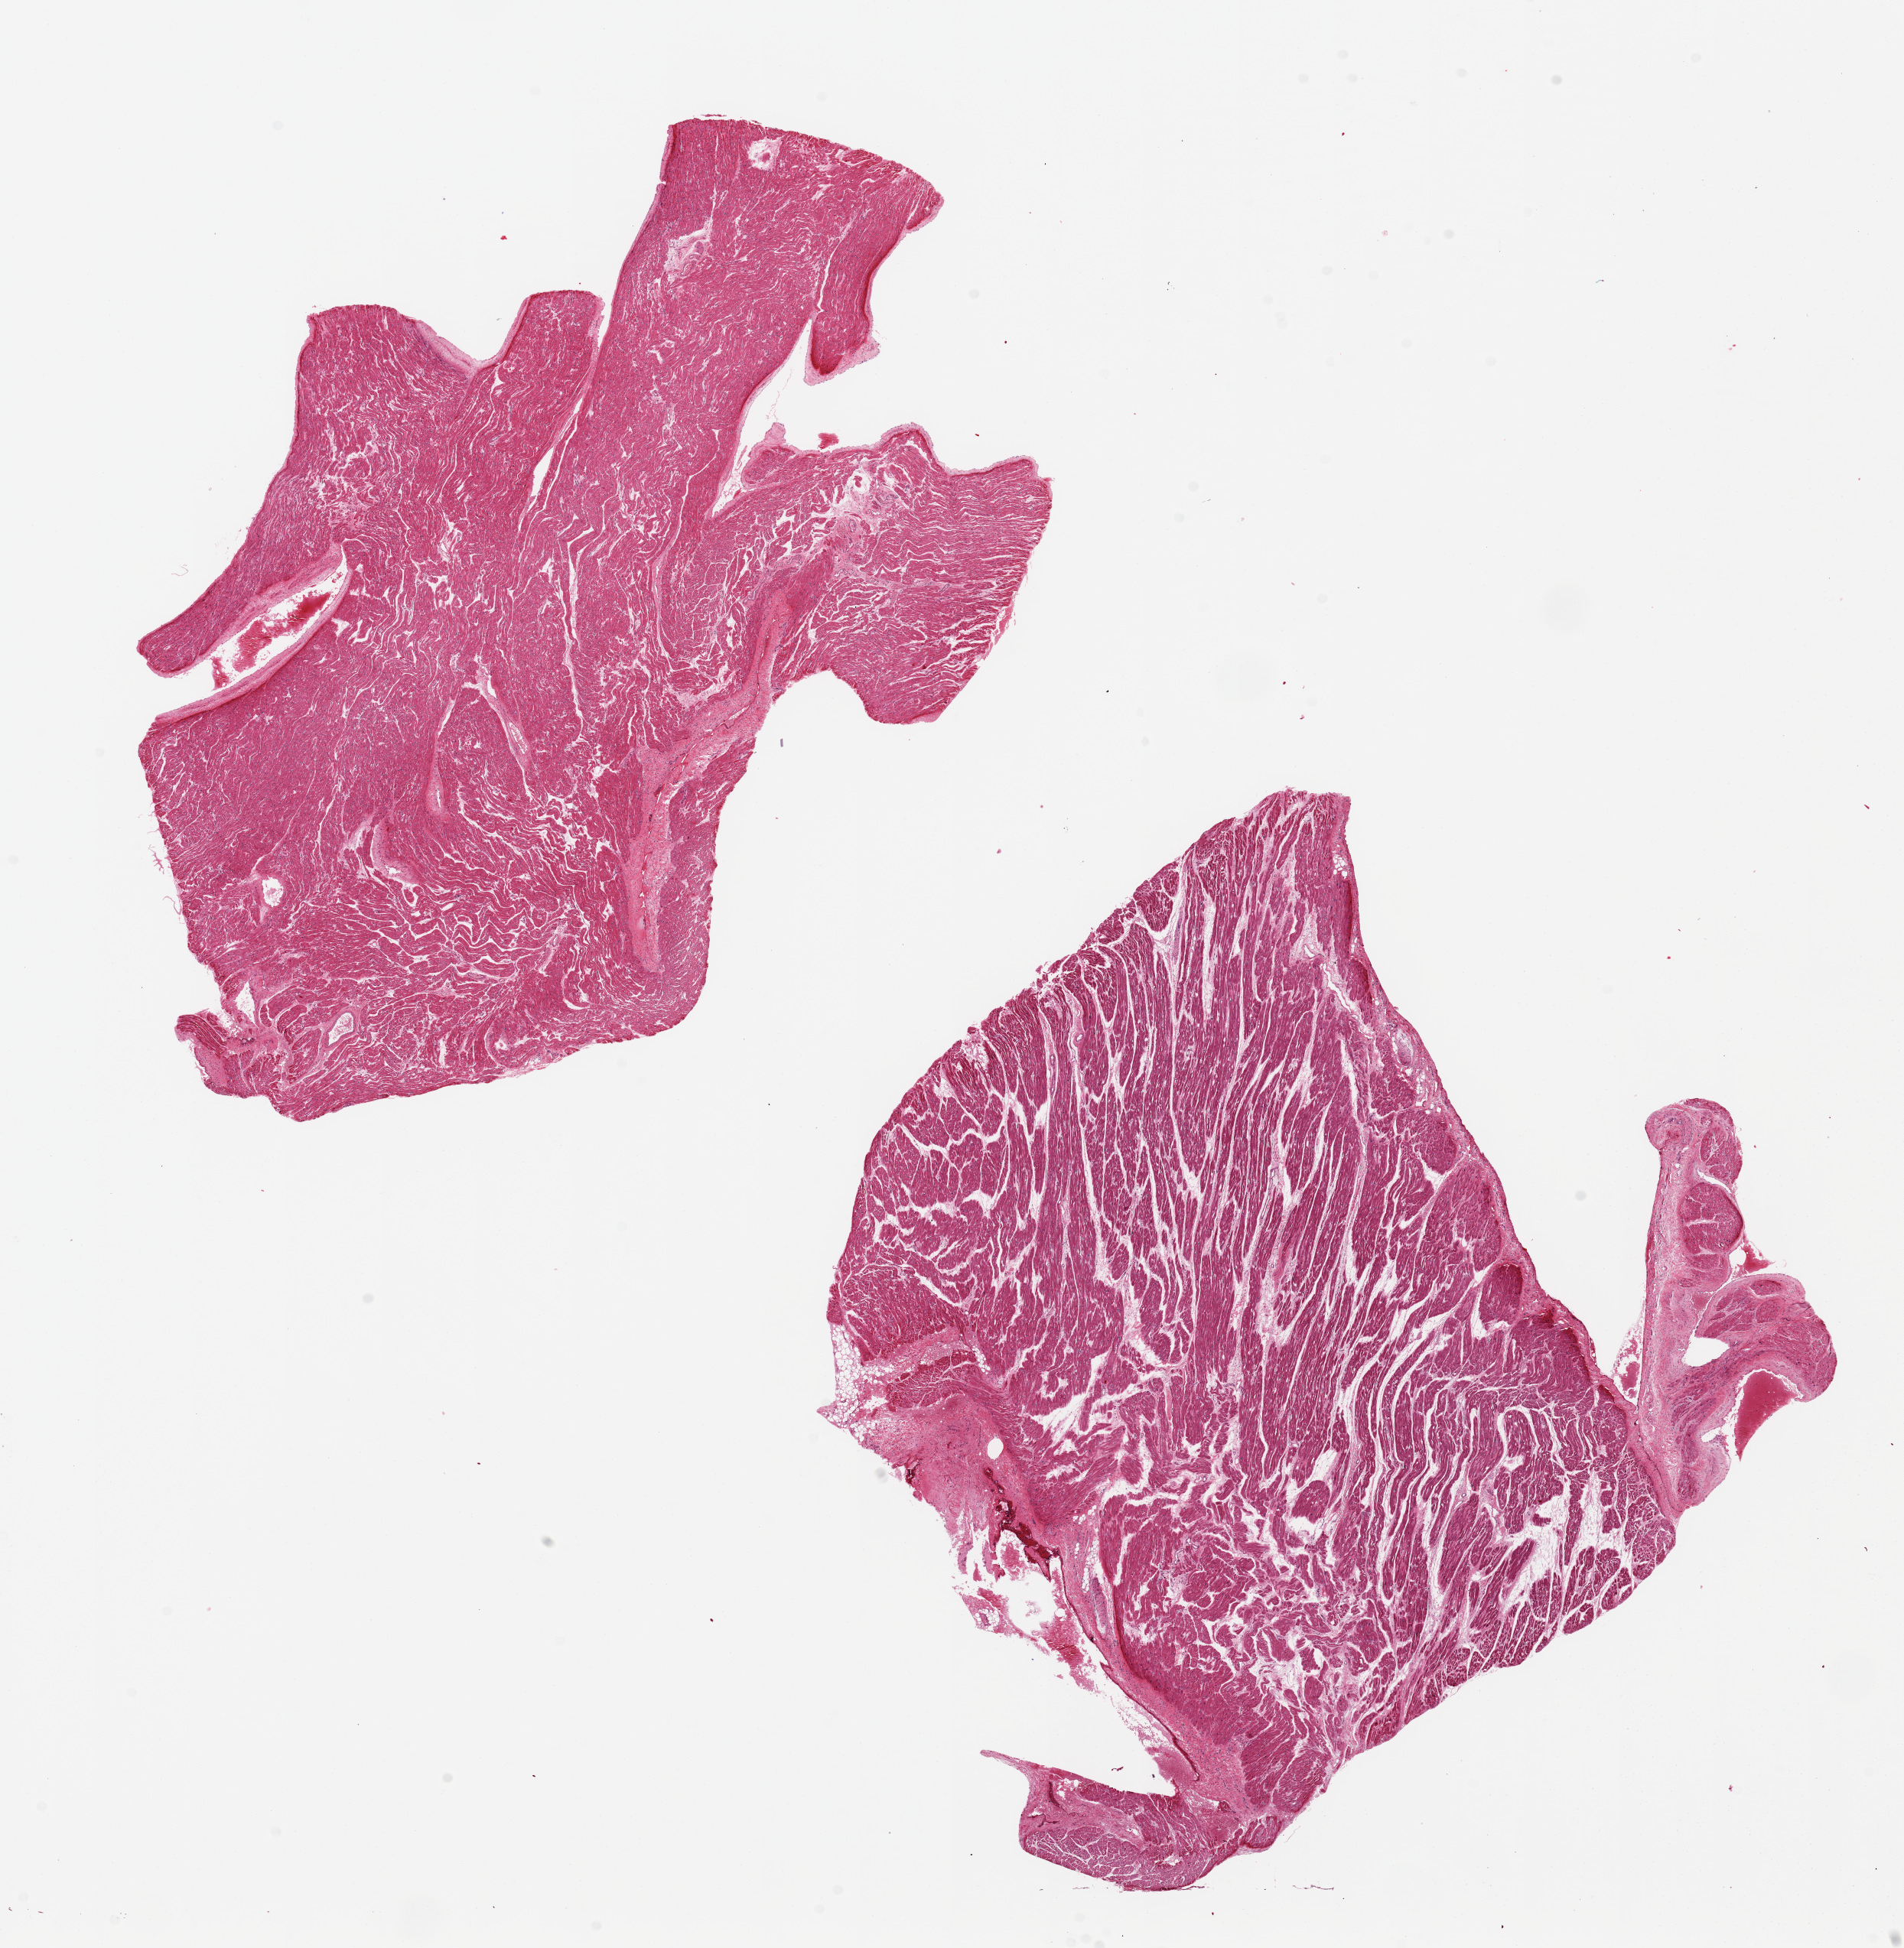
Haematoxylin and eosin whole-slide image, low-resolution overview of the scanned area, about 19.7 x 20.1 mm; PAXgene-fixed, paraffin-embedded tissue; target tissue: auricular appendage; tissue donor sample. Donor sex: female.
Reviewer comment on this tissue sample: 2 pieces, 11x8 & 10x9mm; slight edema.